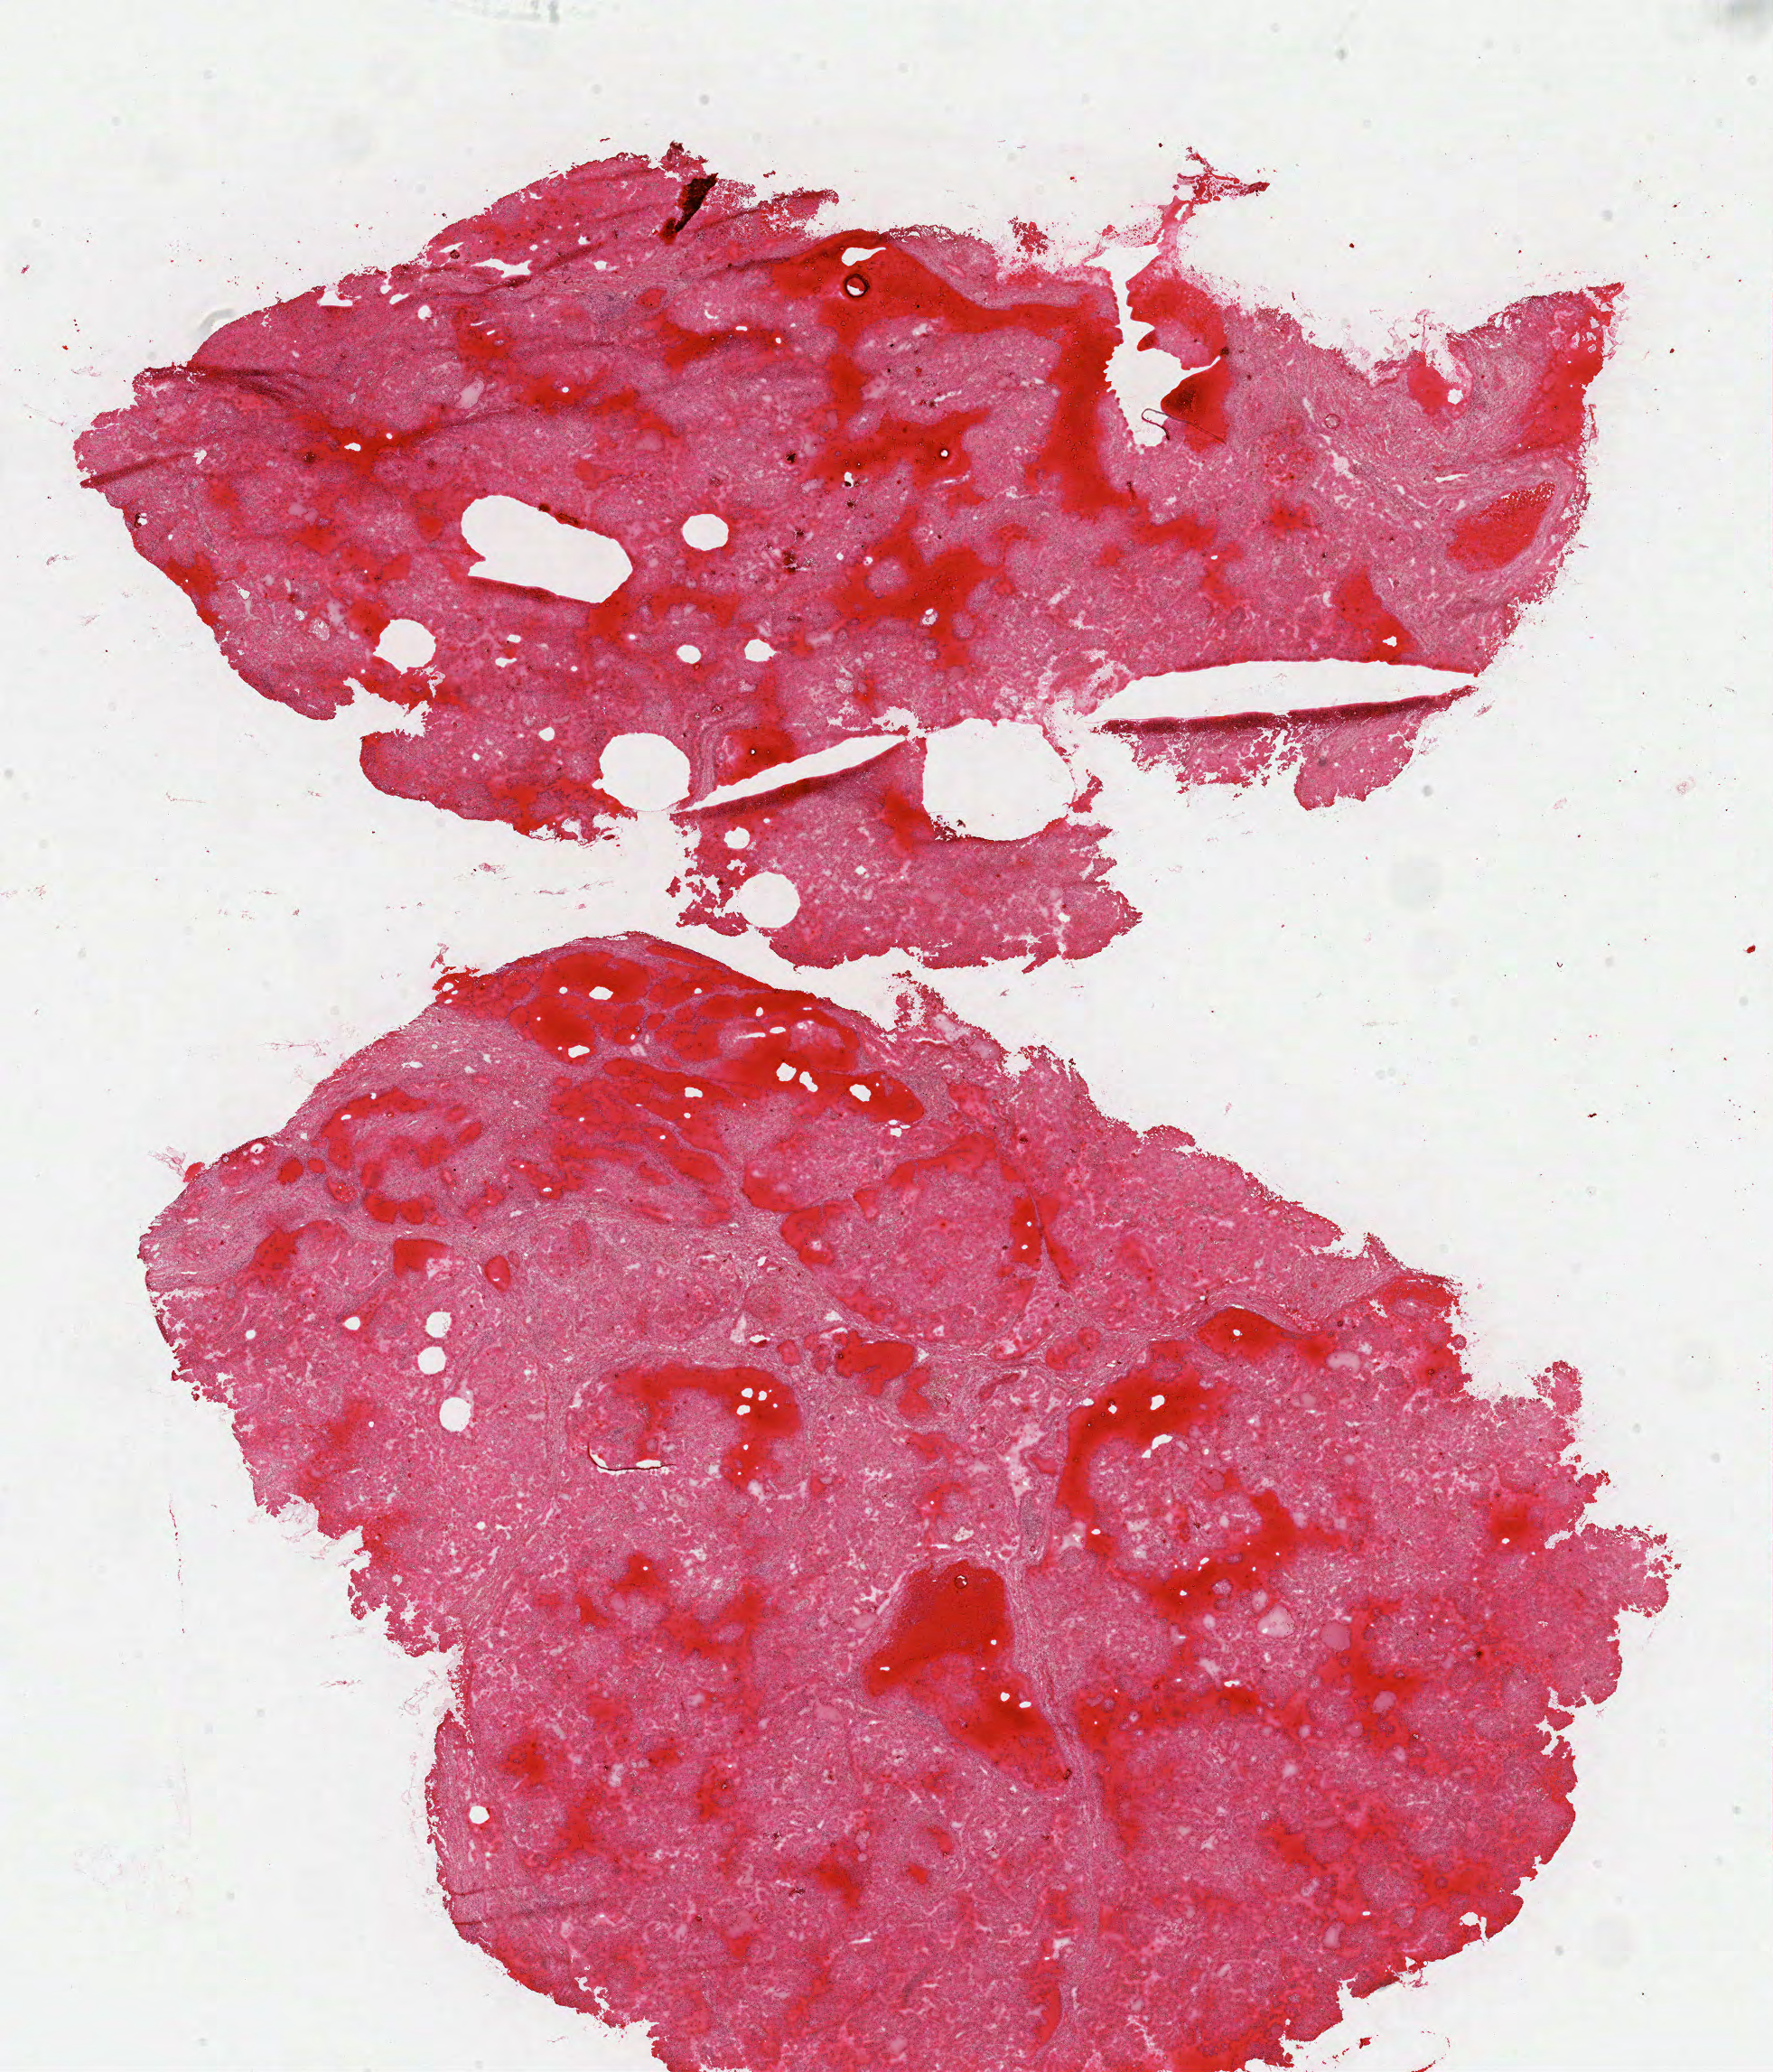
Digitized H&E tissue section (whole slide), whole scanned area (about 15.5 x 18.1 mm, acquisition: 40x scan) shown as a low-resolution overview; frozen section from the top of the tissue portion; kidney, primary tumour sample. Patient: male, age at initial diagnosis 79 years. Pathologist review of this section (percent, as recorded): tumour cells 90%, tumour nuclei 80%, normal cells 0%, stromal cells 10%, necrosis 0%.
AJCC pathologic stage: III. Laterality: left. Histologic diagnosis: Papillary adenocarcinoma, NOS.